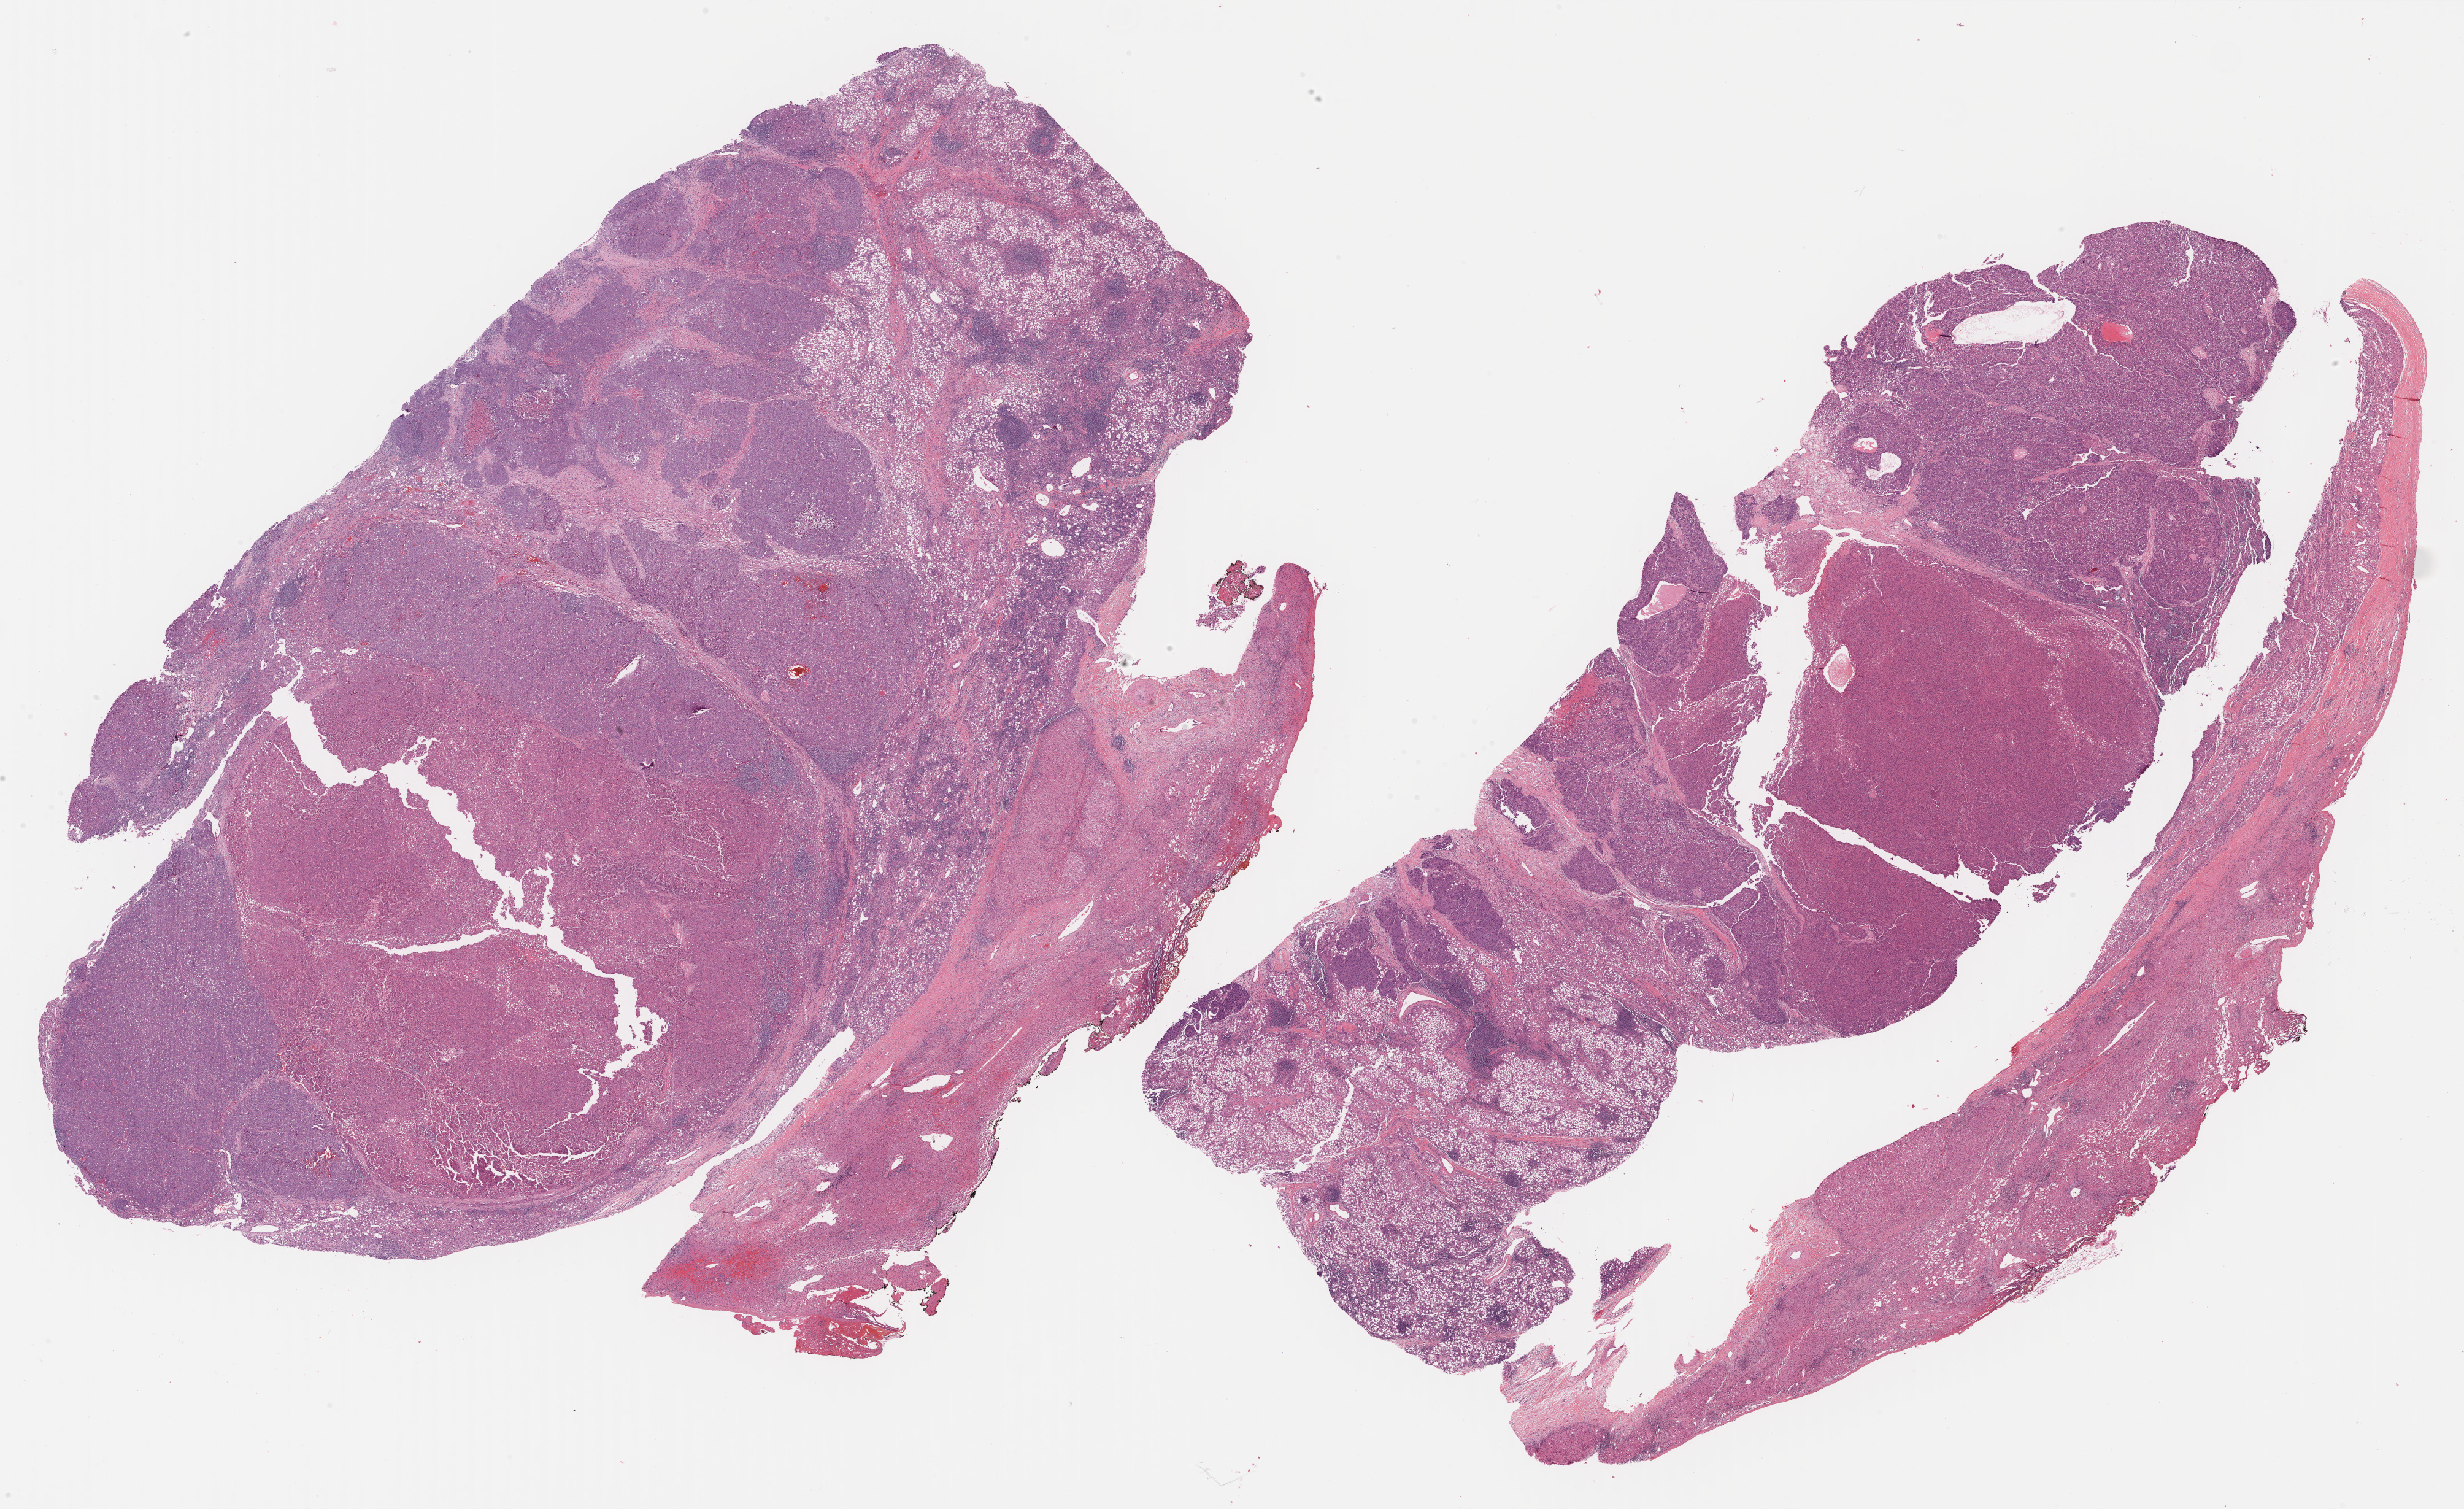
Hematoxylin and eosin (H&E) stained whole-slide image — low-resolution overview of the scanned area, about 32.5 x 19.9 mm (from a 40x scan). Formalin-fixed paraffin-embedded (FFPE) diagnostic section. Liver, primary tumour sample. Patient: female, age at initial diagnosis 57 years. Histologic grade: G3 (poorly differentiated).
AJCC pathologic stage: I (6th edition). Histologic diagnosis: Hepatocellular carcinoma, NOS.